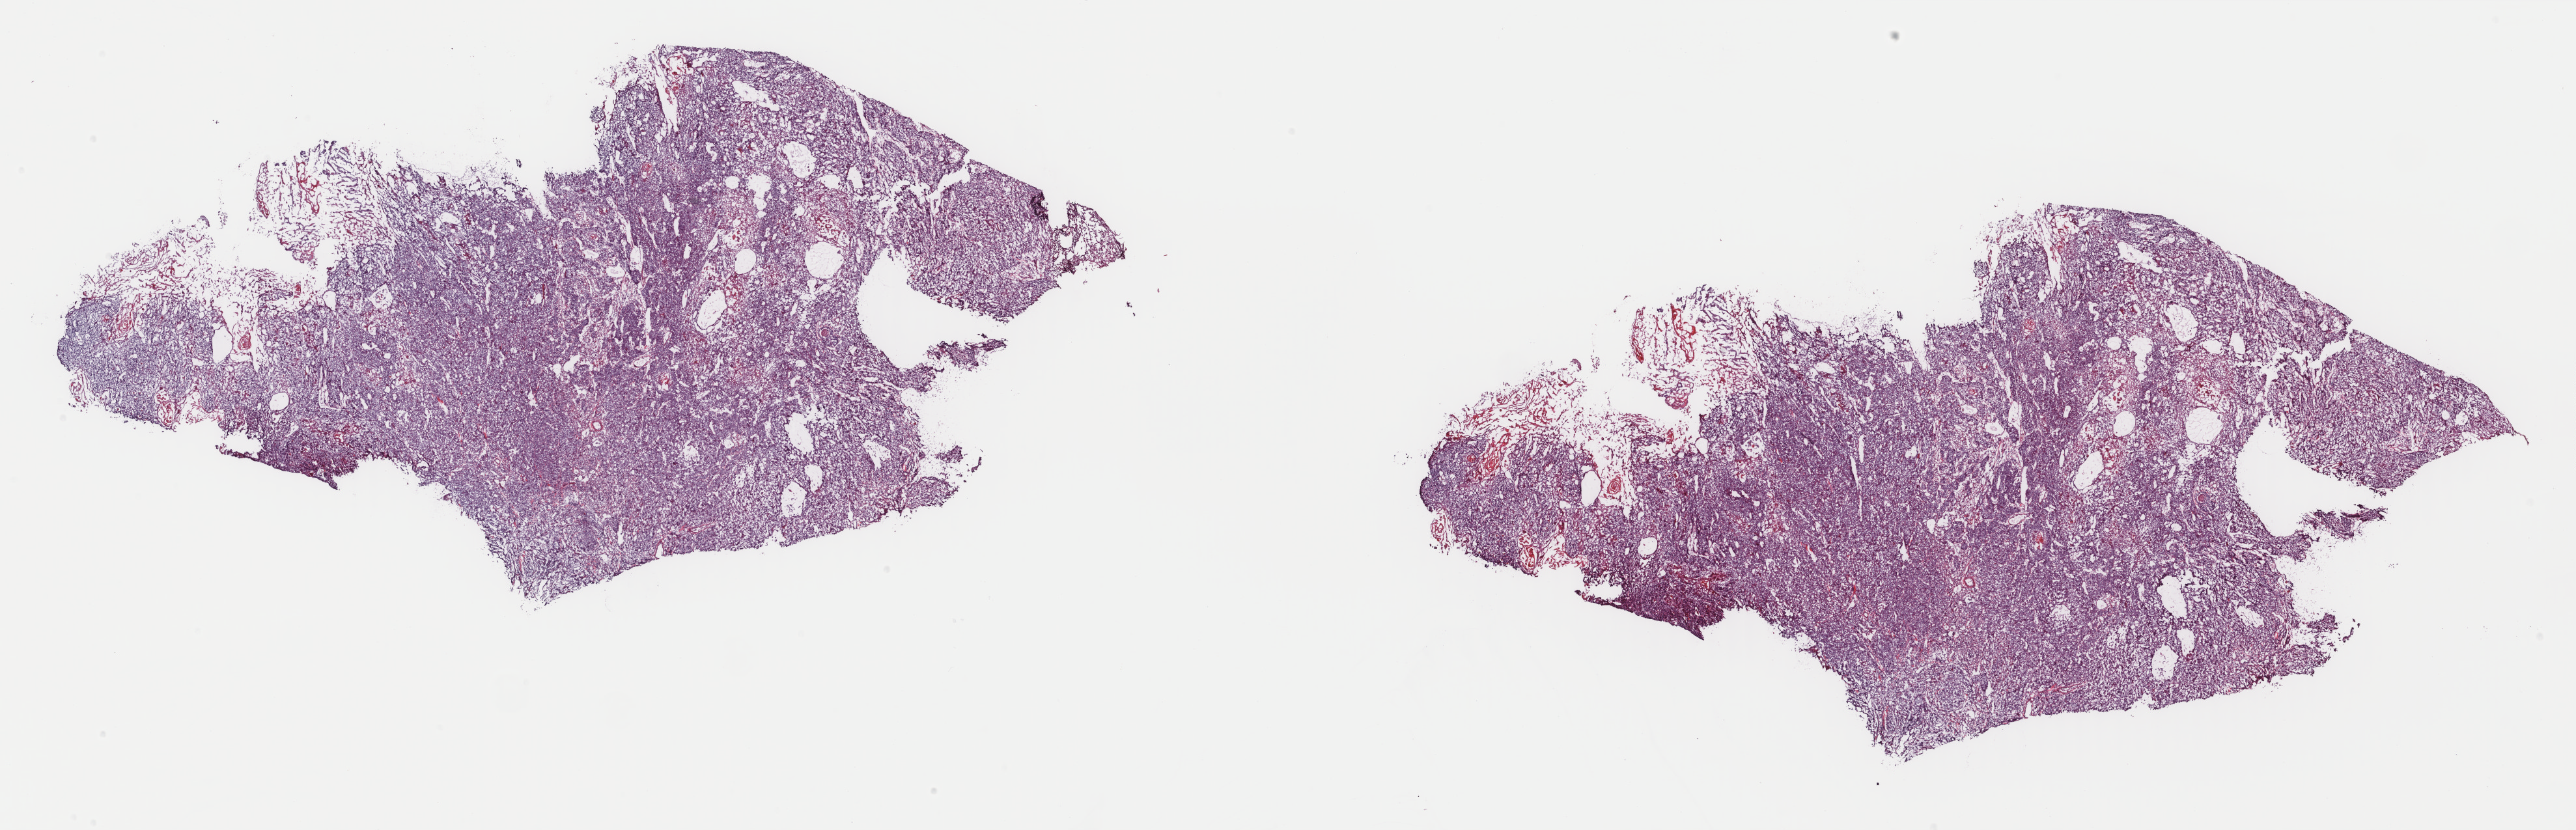
H&E-stained whole-slide image, shown as a low-resolution overview of the whole scanned area (about 31.4 x 10.1 mm); frozen section from the top of the tissue portion; sample: primary tumour, head and neck. Male patient; age at initial diagnosis 51 years. Histologic grade: G2 (moderately differentiated). Slide review estimates, as recorded: tumour cells 90%, tumour nuclei 100%, normal cells 0%, stromal cells 10%, necrosis 0%. Inflammatory infiltration, as recorded: lymphocyte infiltration 6%, monocyte infiltration 2%, neutrophil infiltration 0%.
AJCC pathologic stage: IVA (7th edition). Pathologic diagnosis: Squamous cell carcinoma, keratinizing, NOS. Laterality: left. Lymph nodes positive (case pathology): 4 of 9 examined.